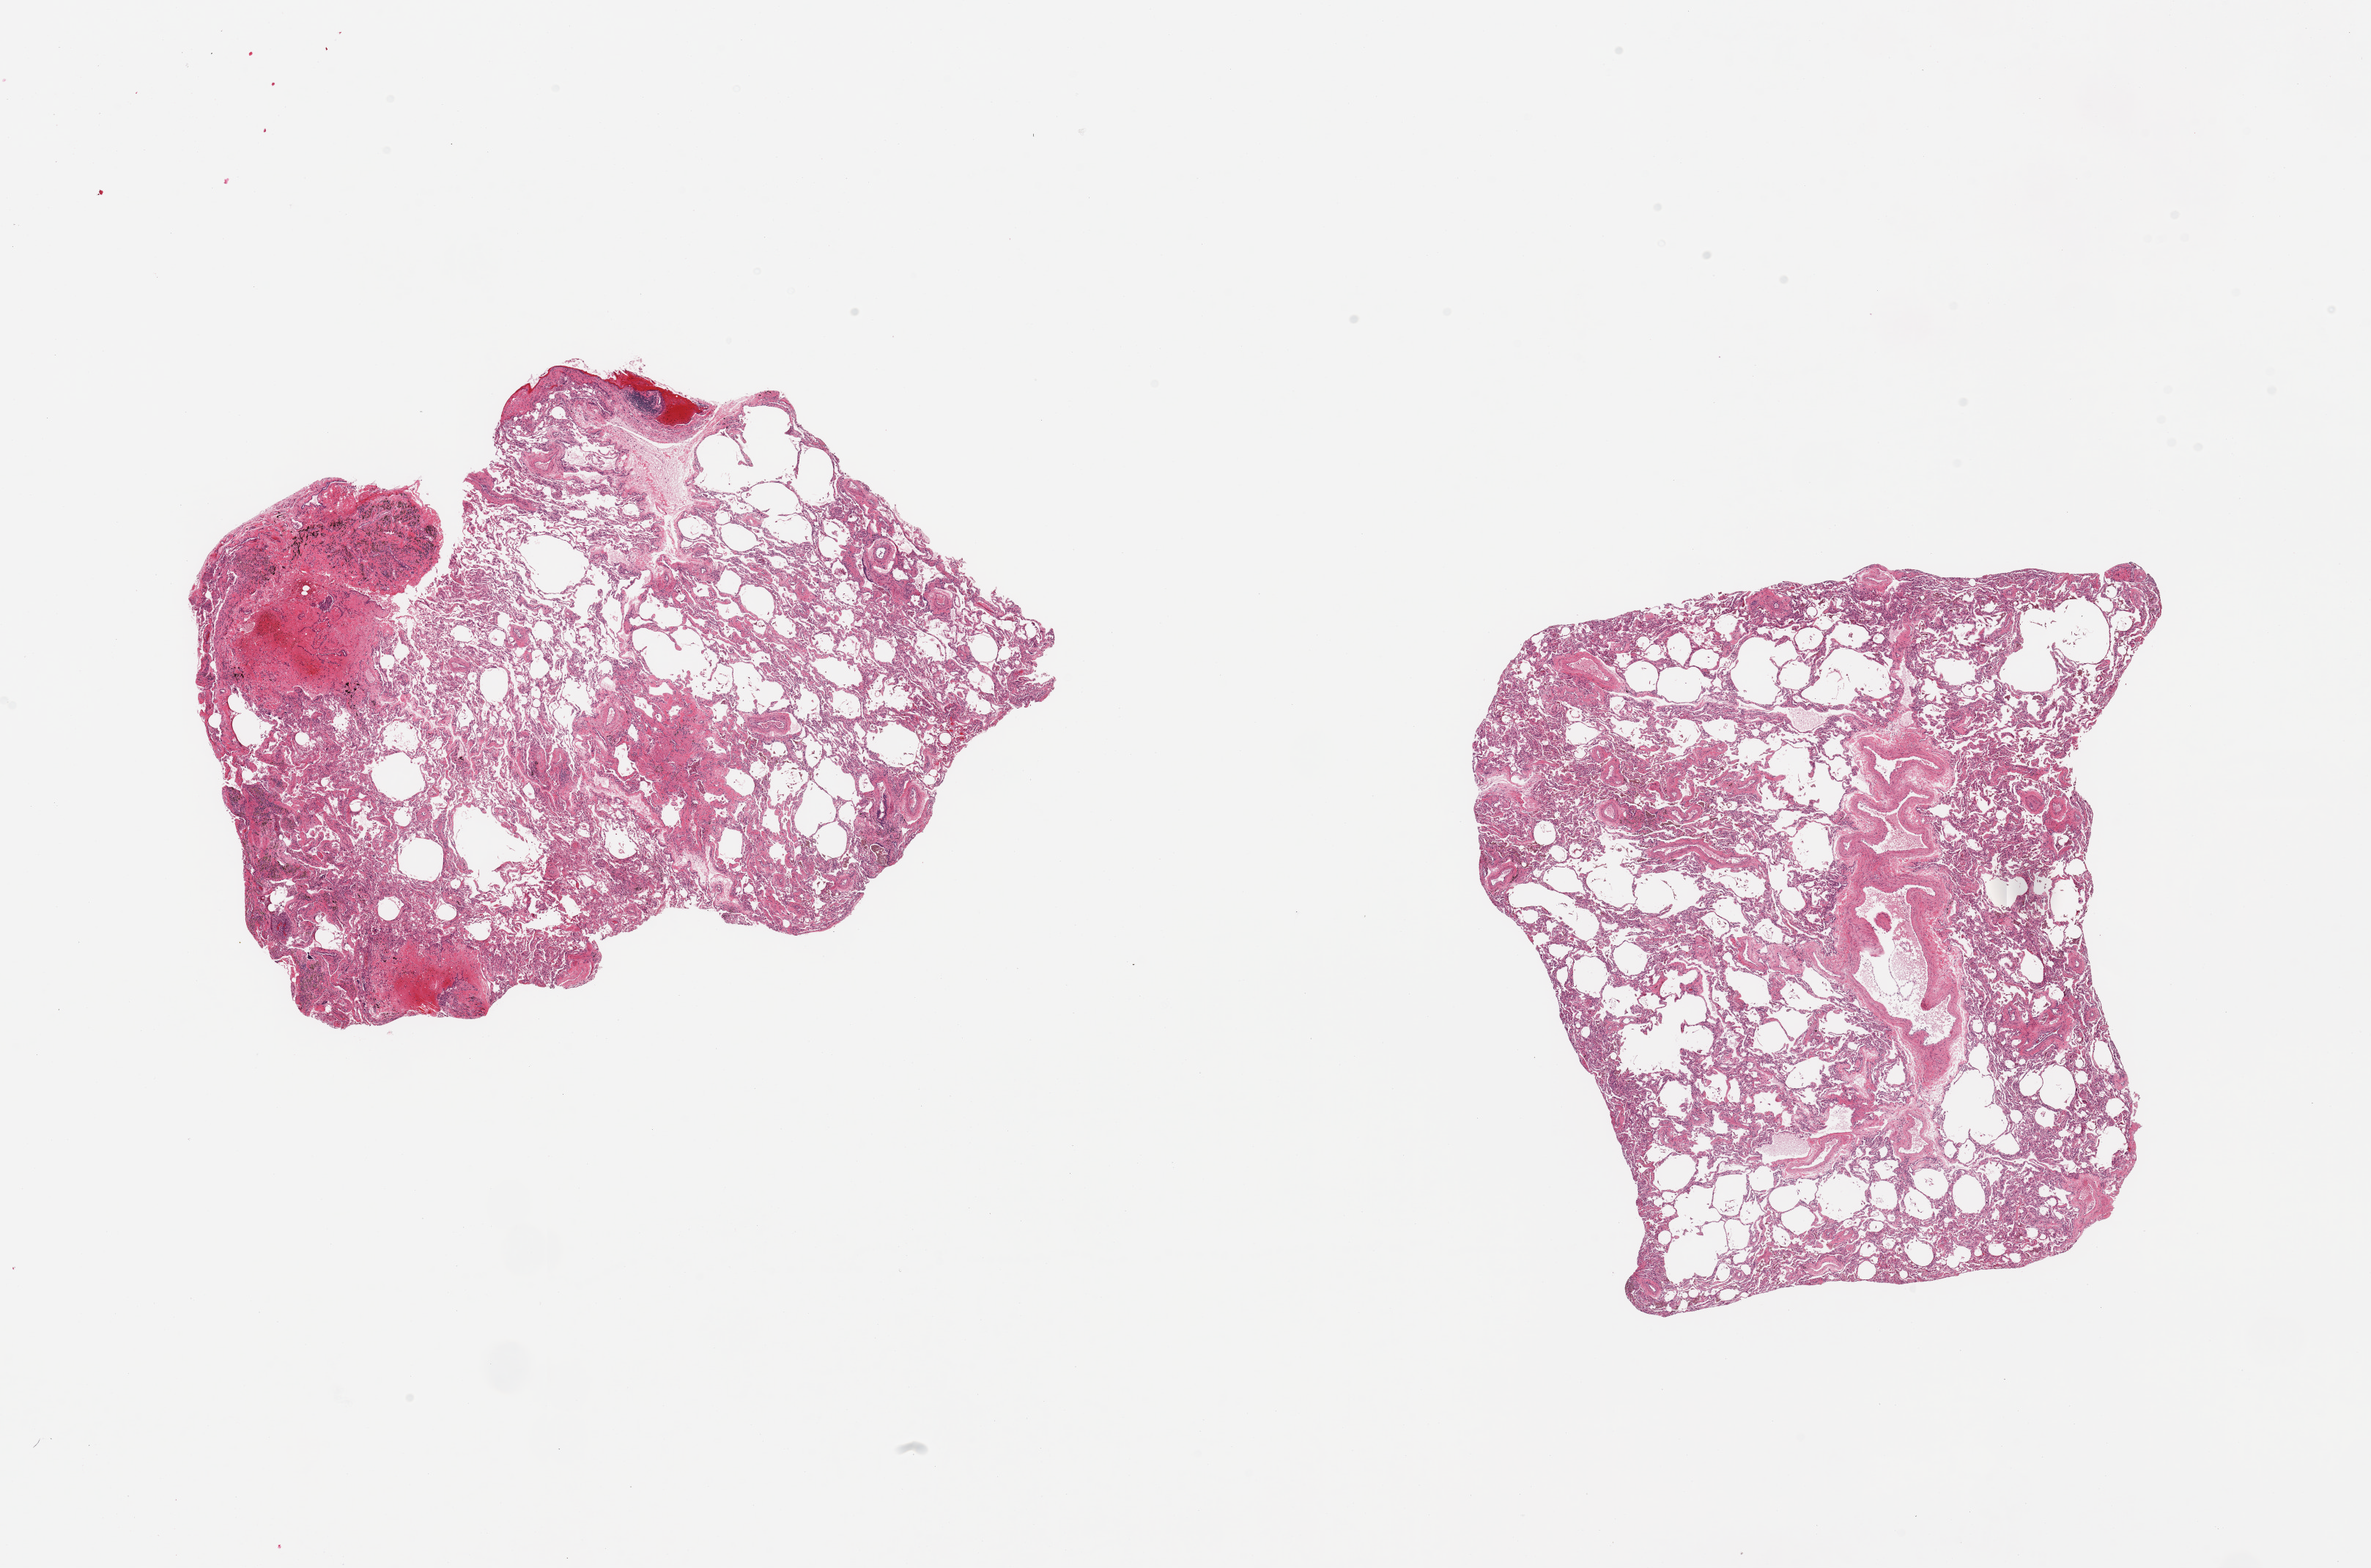
Whole-slide image, hematoxylin and eosin (H&E) stain, brightfield — a low-resolution overview of the entire scanned area, about 25.6 x 16.9 mm, PAXgene-fixed, paraffin-embedded tissue, target tissue: lung, donor tissue sample. Donor sex: male.
Review note (as recorded): 2 pieces; patchy emphysema and fibrosis with foci of recent hemorrhage.